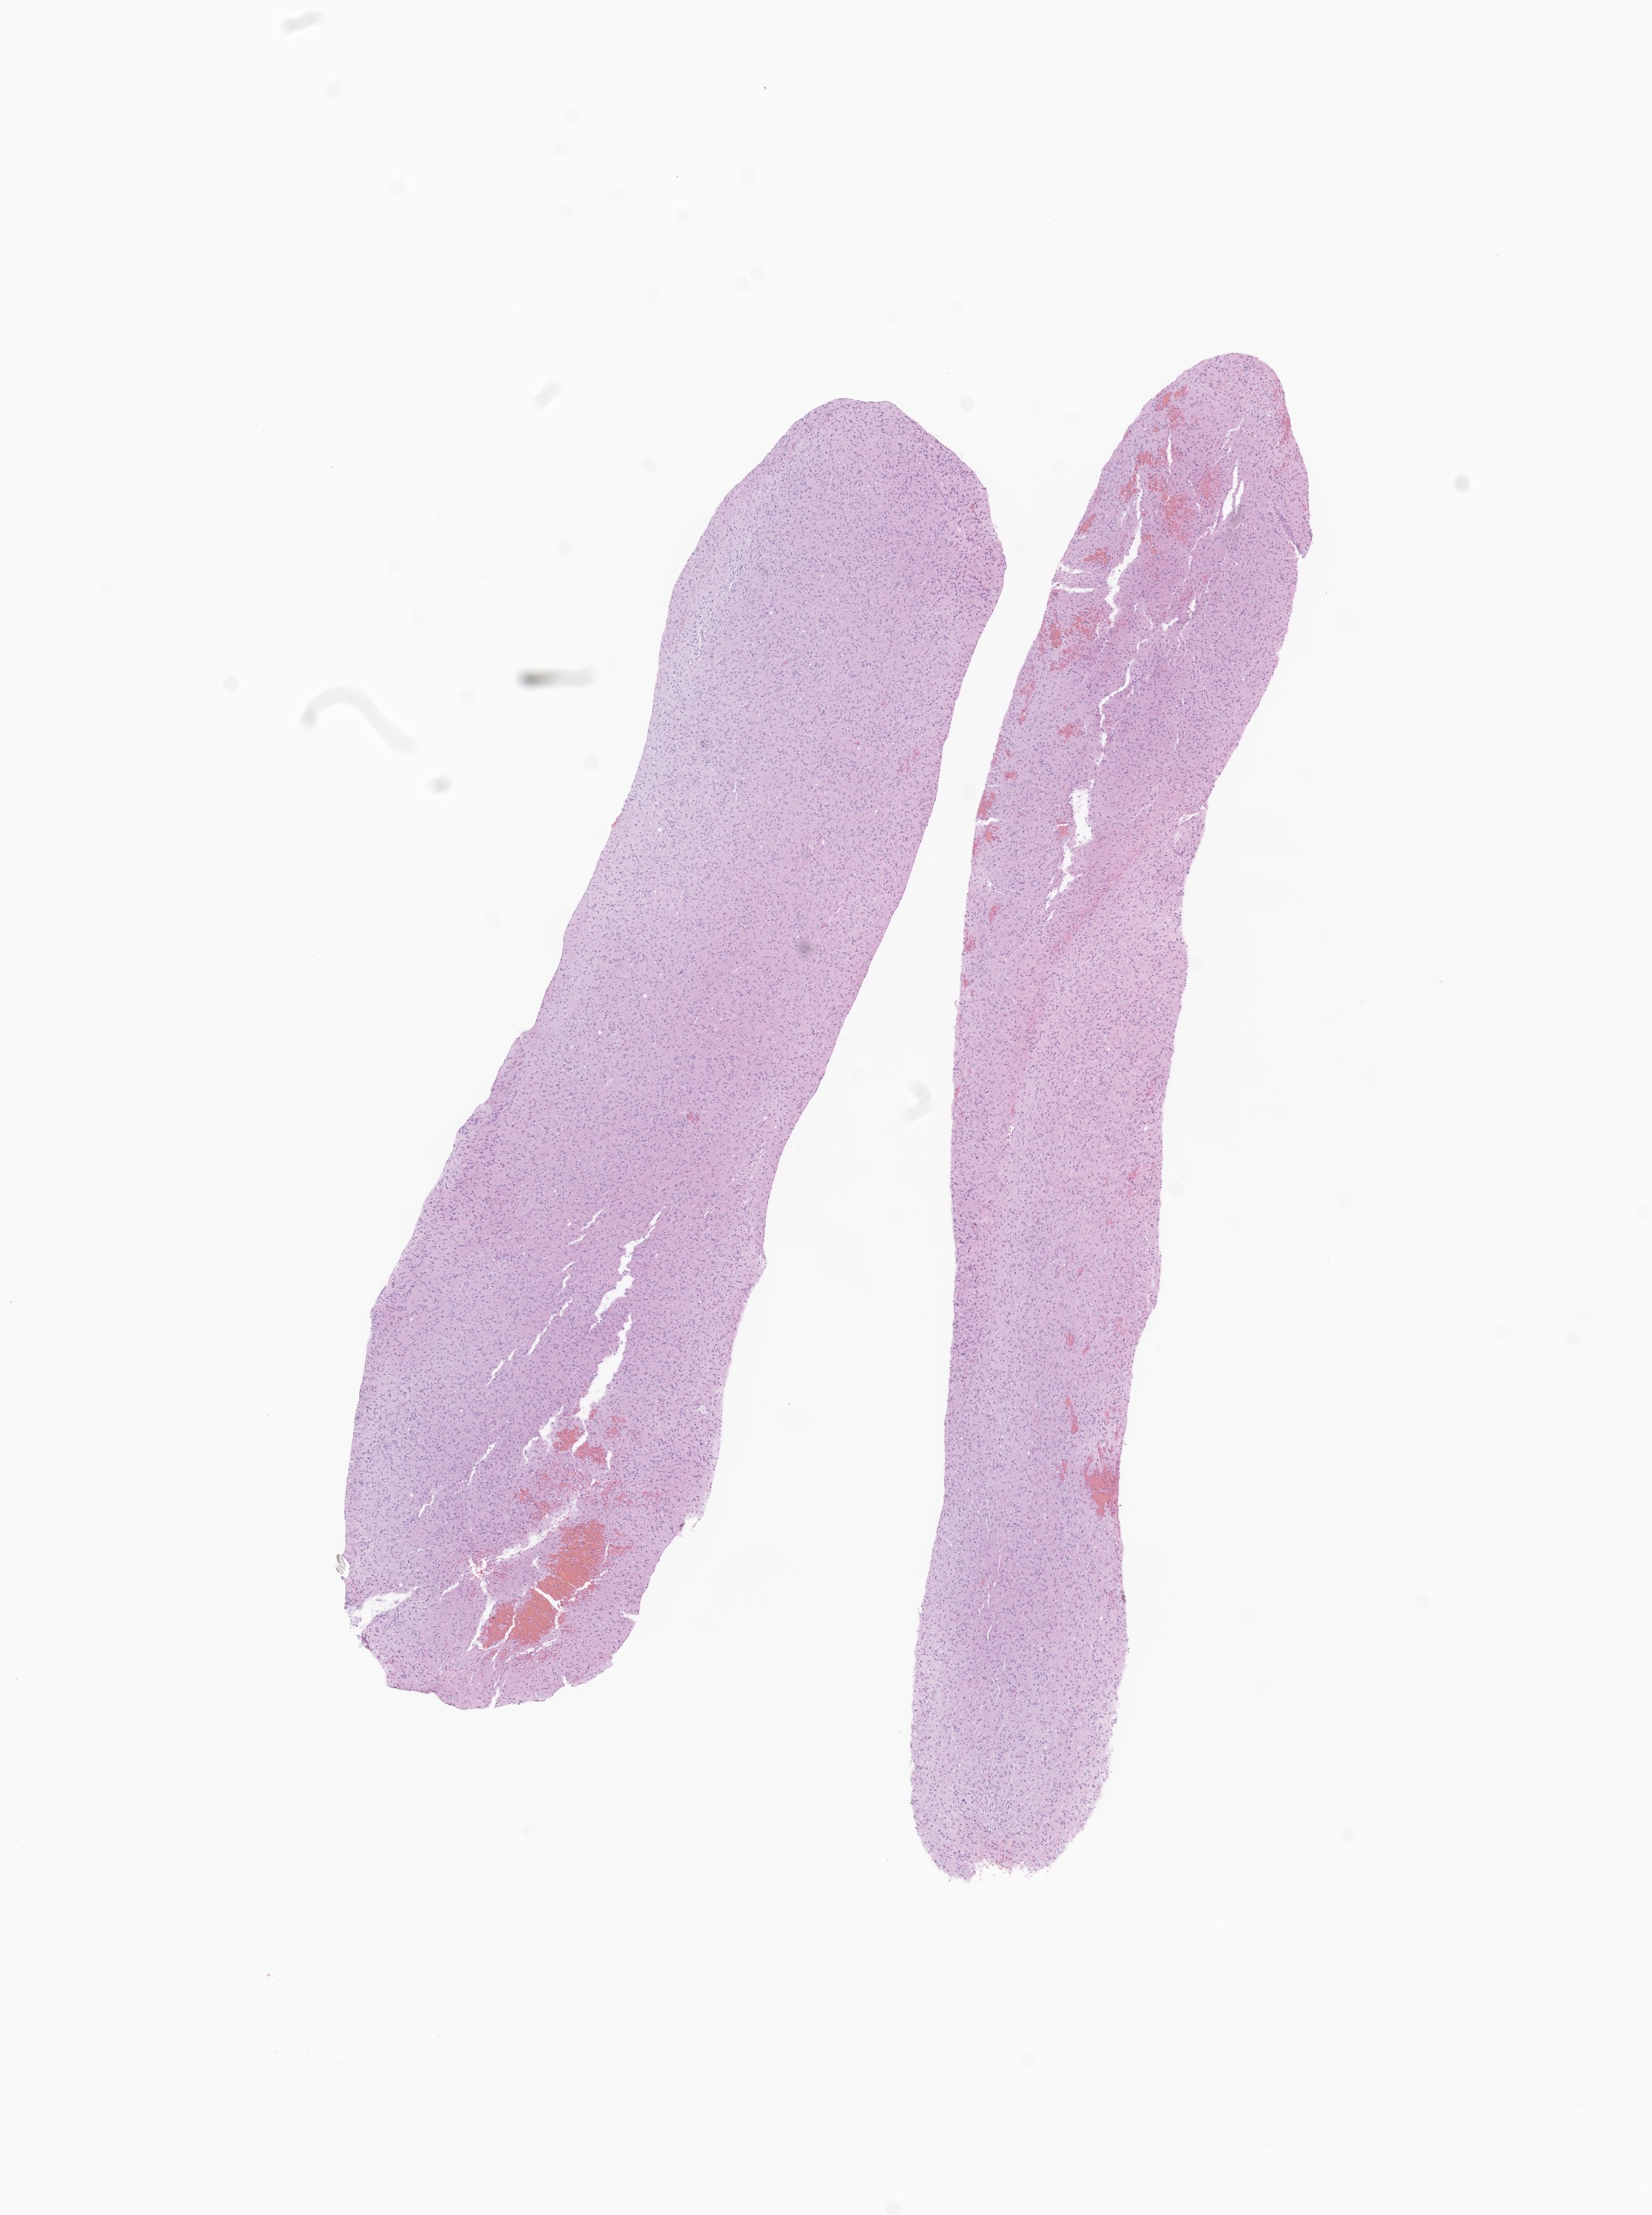
Digitized hematoxylin and eosin (H&E)-stained section of tumor tissue from the brain, whole scanned area (about 9.0 x 12.1 mm) shown as a low-resolution overview, formalin-fixed paraffin-embedded section. Male patient, age 81 months (6 years 9 months).
Diagnosis (ICD-O-3 morphology term): Glioma, malignant.